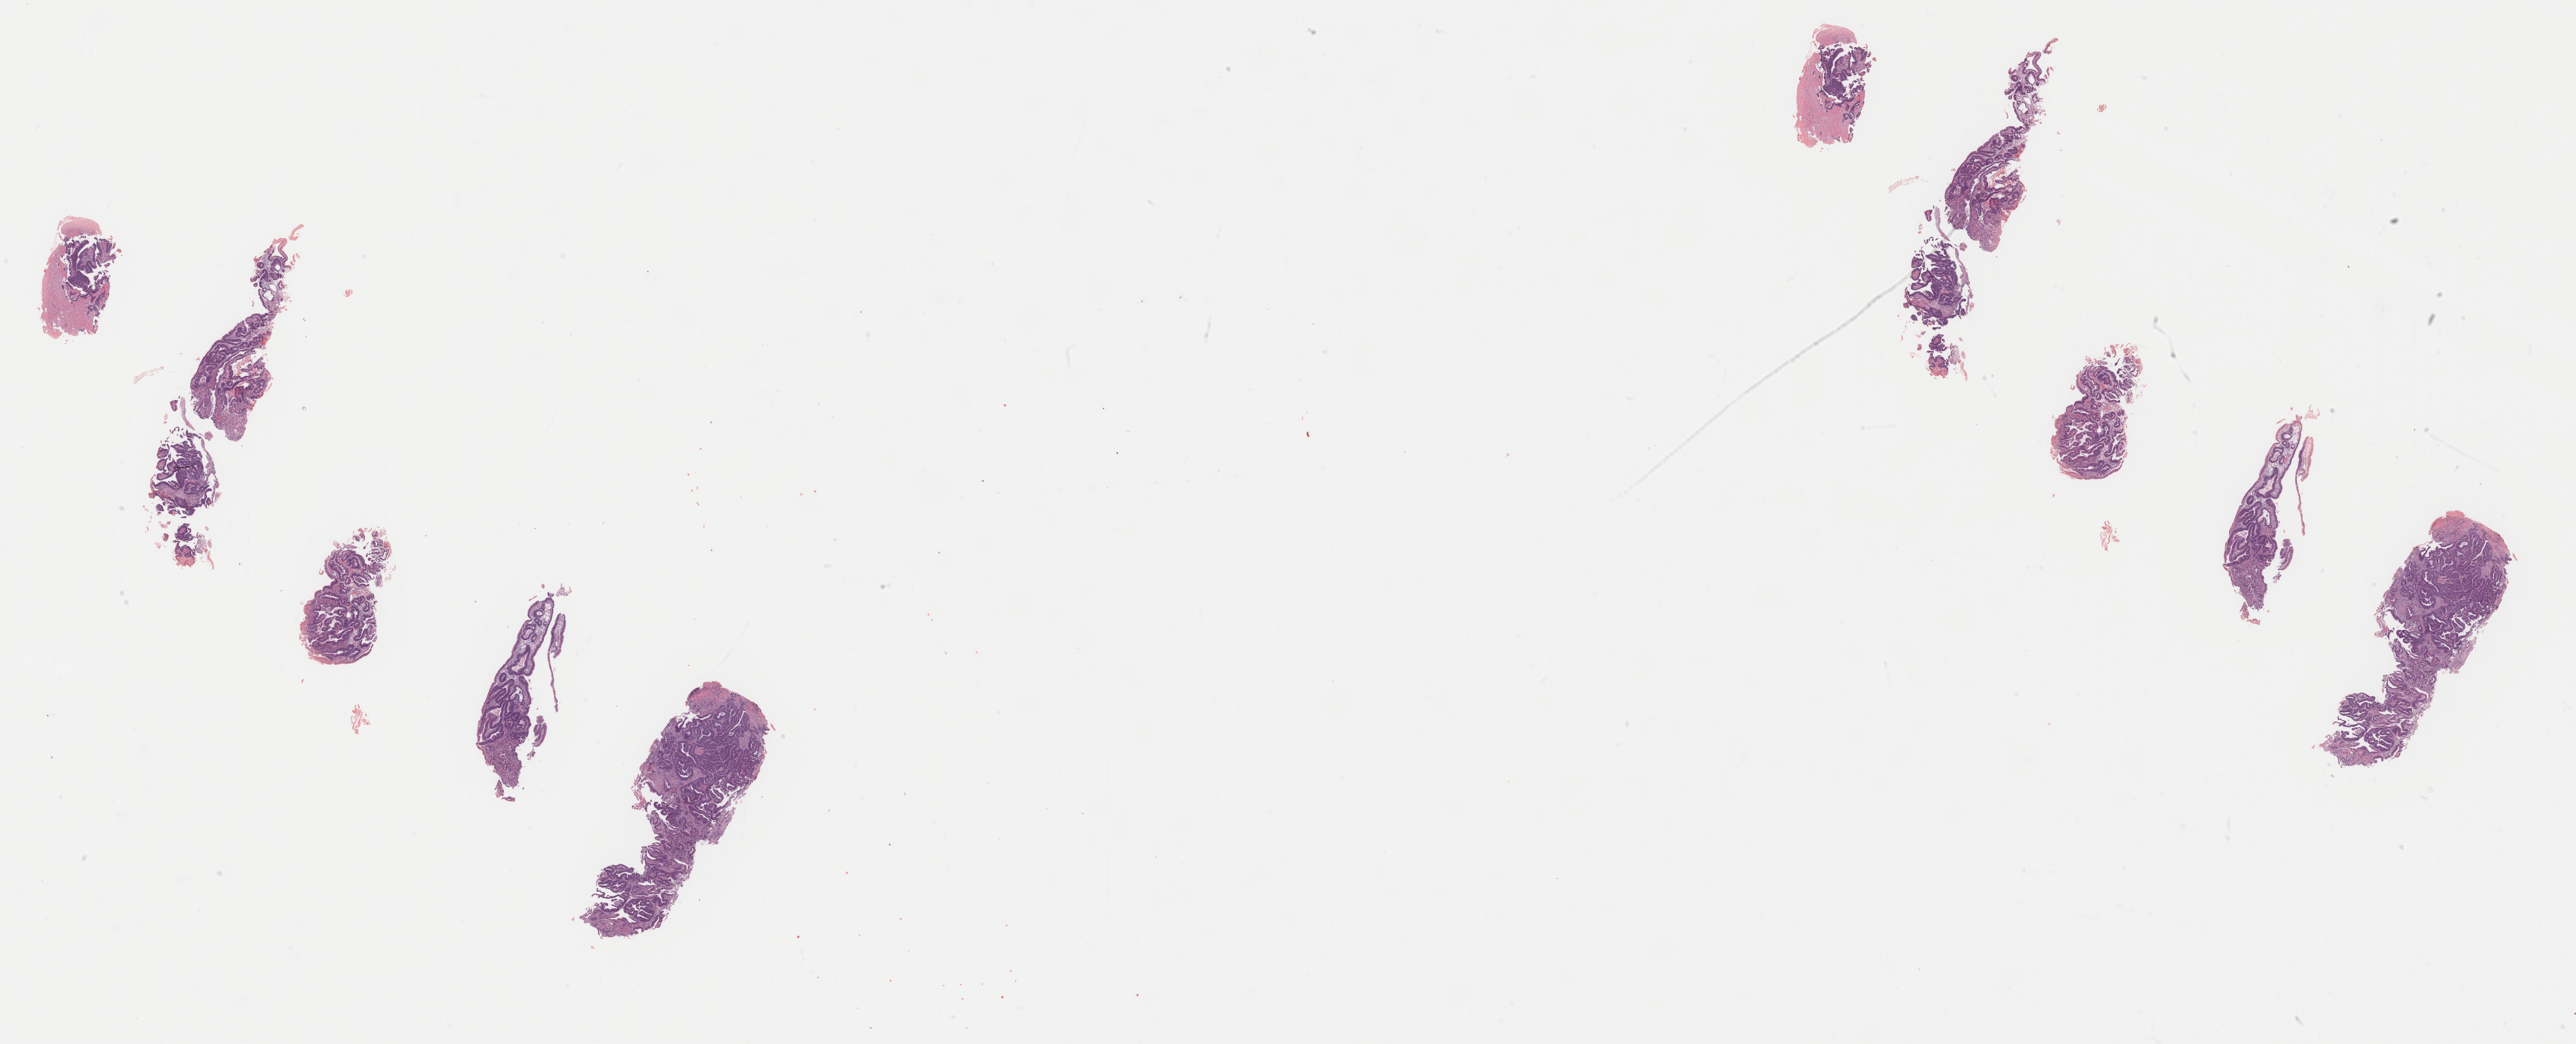
Digitized Hematoxylin and eosin (H&E) stained tissue section (whole slide) — whole scanned area (about 32.1 x 13.0 mm, acquisition: 40x scan) shown as a low-resolution overview; FFPE section; primary tumour sample from the esophagus. Male patient; age at initial diagnosis 71 years. Histologic grade: G3 (poorly differentiated). Slide review estimates, as recorded: tumour cells 85%, tumour nuclei 90%, normal cells 0%, stromal cells 15%, necrosis 0%. Infiltration values recorded for this section: lymphocyte infiltration 4%, monocyte infiltration 5%, neutrophil infiltration 4%.
* diagnosis: Adenocarcinoma, NOS (lower third of esophagus)